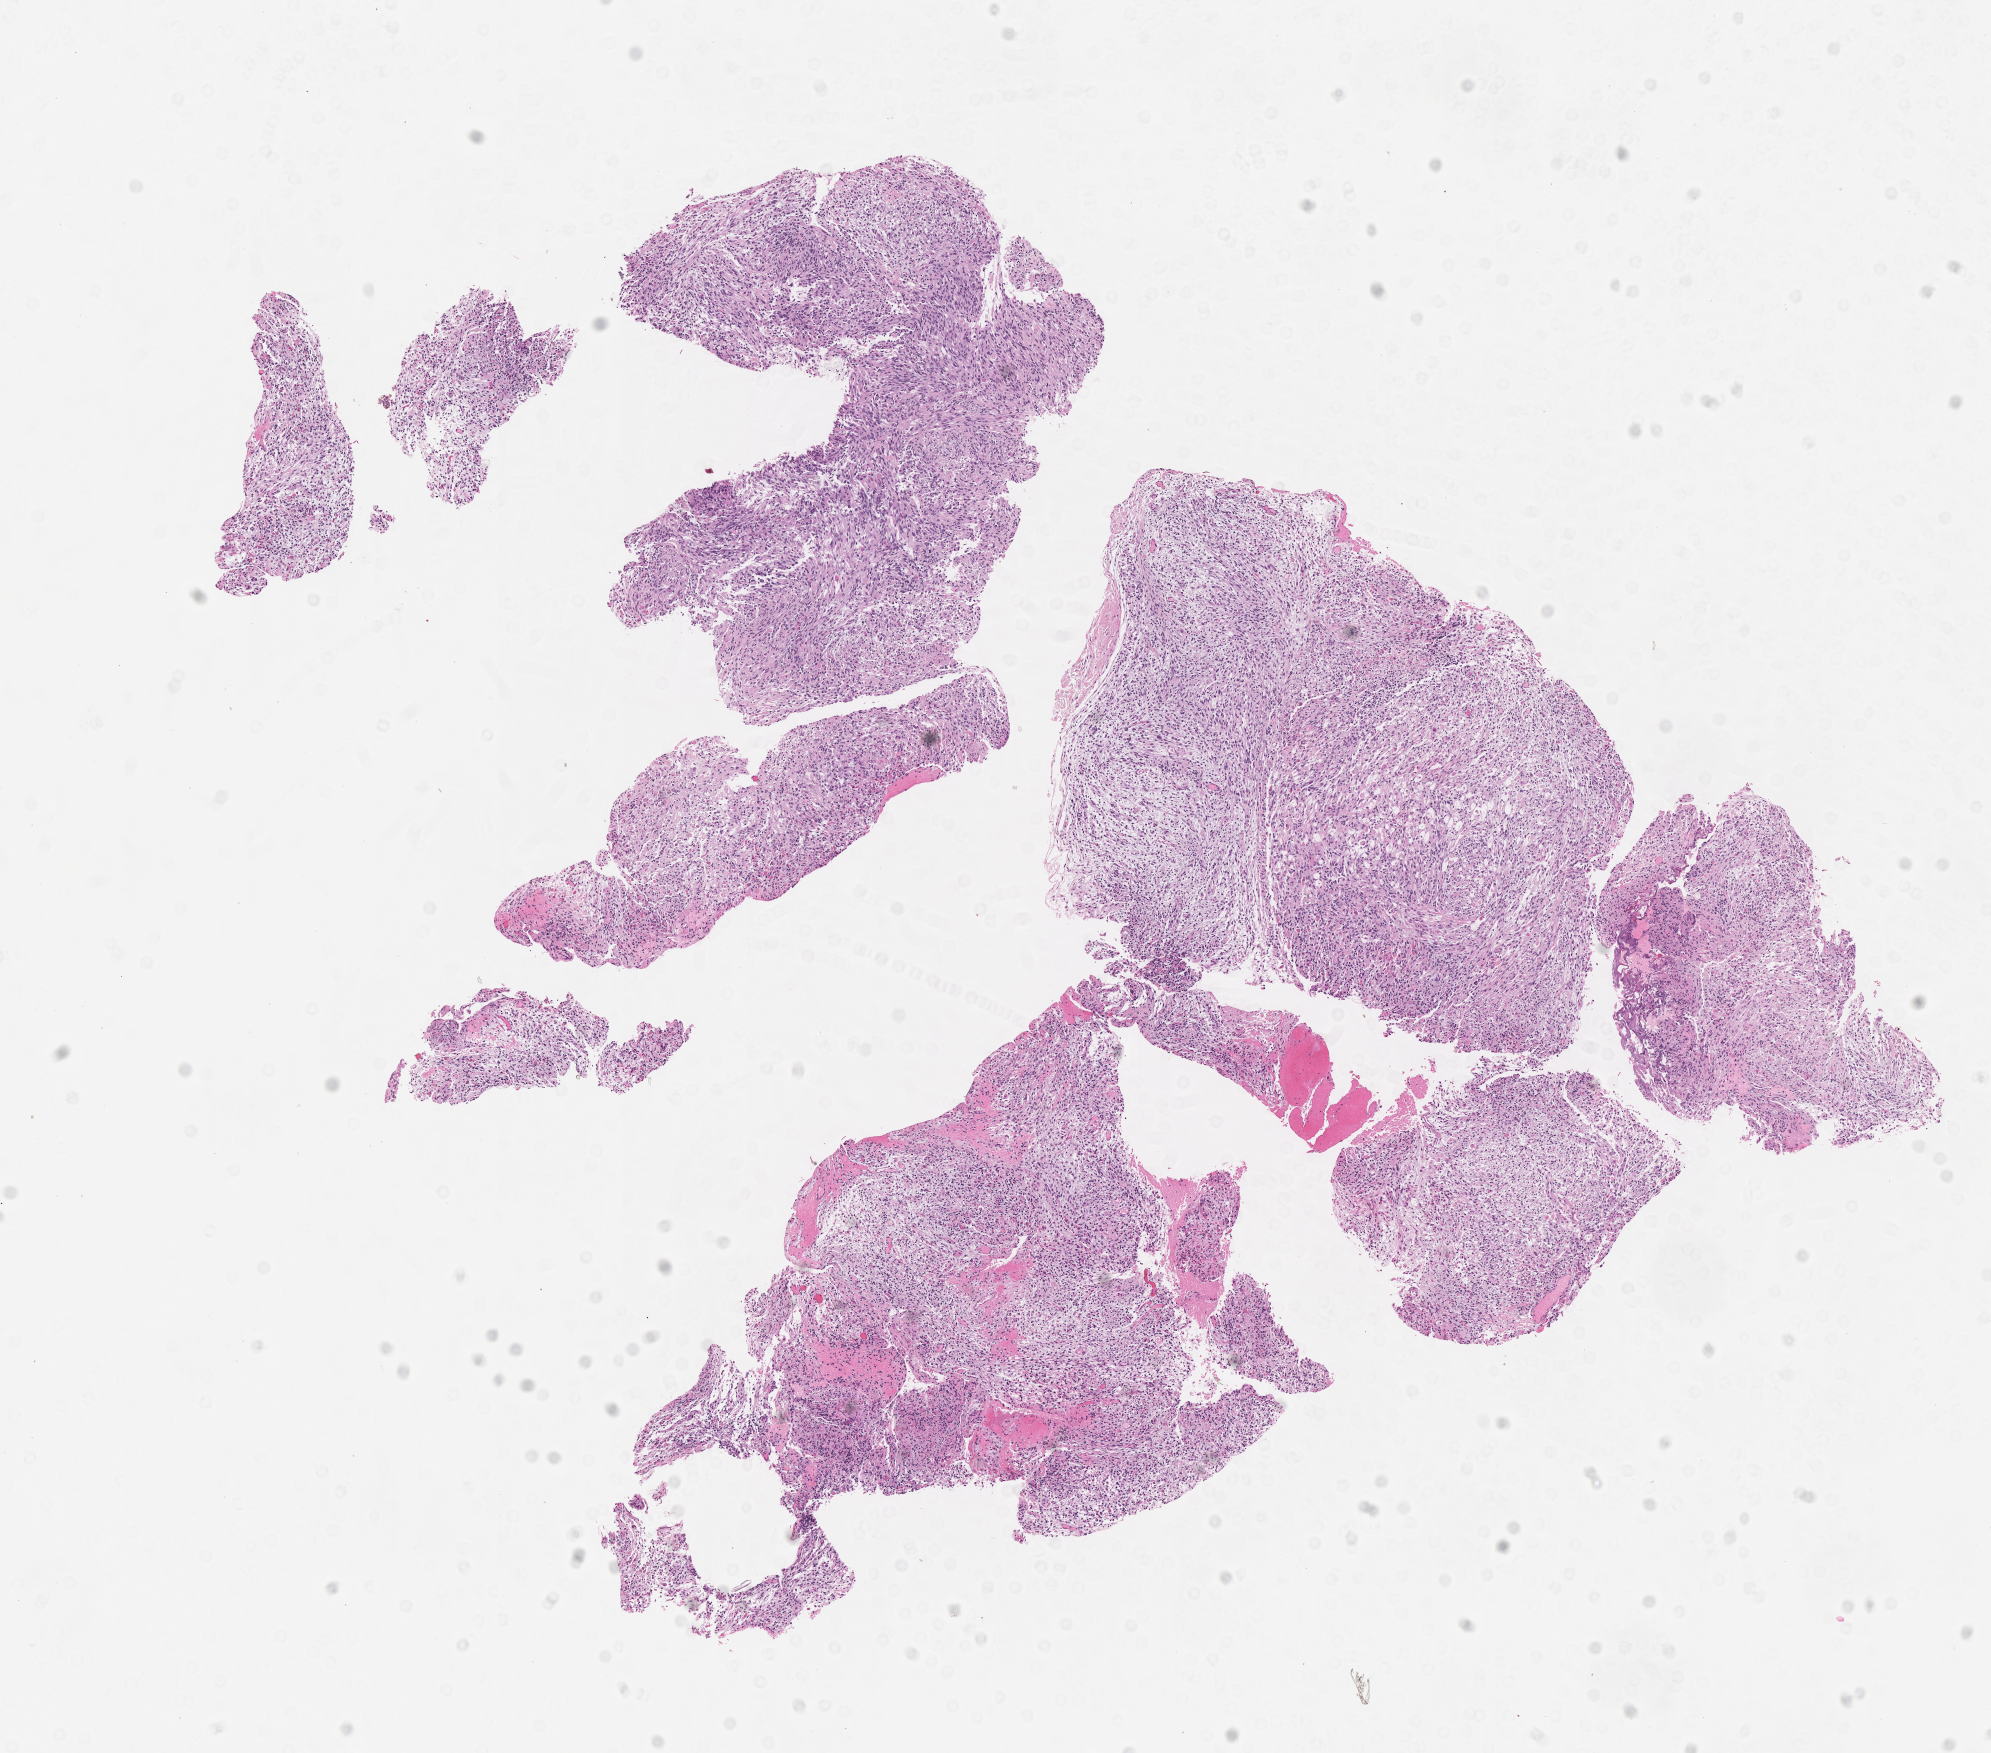
Haematoxylin and eosin whole-slide image of tumor tissue — whole scanned area (about 8.1 x 7.1 mm) shown as a low-resolution overview, formalin-fixed paraffin-embedded section, sample anatomic site: eye - orbit, right. Patient: female, age 5.6 years at diagnosis.
Metastatic status at presentation (as recorded): non-metastatic (unconfirmed). Diagnosis: rhabdomyosarcoma; histological classification: embryonal rhabdomyosarcoma. Stage (as recorded): 1.